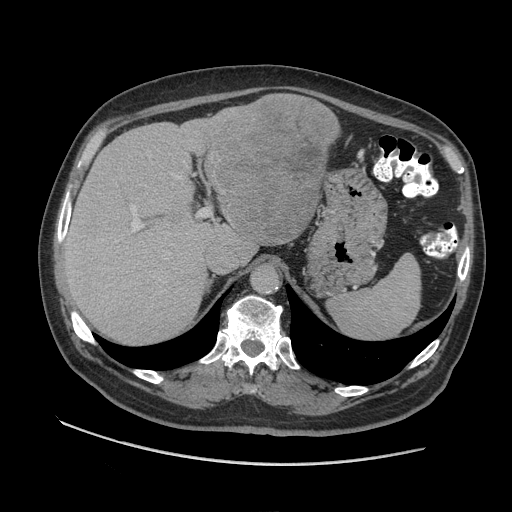
Contrast-enhanced abdominal CT (liver protocol), one axial slice. Slice 65 of 109 in the series (ordered by position). Reconstruction kernel STANDARD. 140 kVp. Soft-tissue window (W 400 / L 40 HU). 2.5 mm slice thickness. 512 × 512 image matrix. Case-level facts recorded for this patient, not image findings: diagnosis: hepatocellular carcinoma (patient treated with transarterial chemoembolisation; whether this scan precedes or follows treatment is not stated here); TNM stage (as recorded): Stage-I; Child-Pugh class: A; tumour nodularity: uninodular.
Structures marked on this image (semi-automatic segmentation, software-assisted and operator-edited):
- liver parenchyma outside the tumour (the mass and vessels are separate outlines, so this box may not span the whole liver): bounding box [x1, y1, x2, y2] px = [64, 106, 332, 342]
- mass: [205, 93, 340, 244]
- liver vessels: [115, 176, 181, 254]